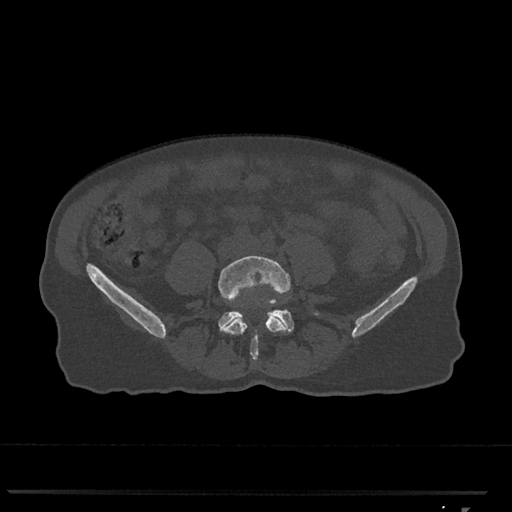
CT including the spine, one axial slice. Slice 183 of 793 in the series (ordered by position). Reconstruction kernel Br40s/3. Bone window (W 1800 / L 400 HU). 0.5 mm slice thickness. 512 × 512 image matrix, field of view 380 × 380 mm. Female patient, age 62 years. From the clinical record (not read from this slice): primary cancer: renal.
Structures marked on this image (semi-automatically segmented with operator editing):
- L4 vertebra: bounding box <218,255,291,361> (left, top, right, bottom; pixels)
- L5 vertebra: <218,299,294,333>